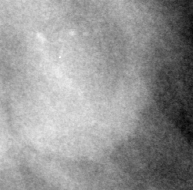
Region of interest cut from a scanned film mammogram (one marked finding); left breast; MLO view.
Finding: mass, shape round, margins circumscribed; BI-RADS assessment category 3; subtlety rating 3 on a 1 (subtle) to 5 (obvious) scale; pathology result (as recorded, not read from the image): benign.